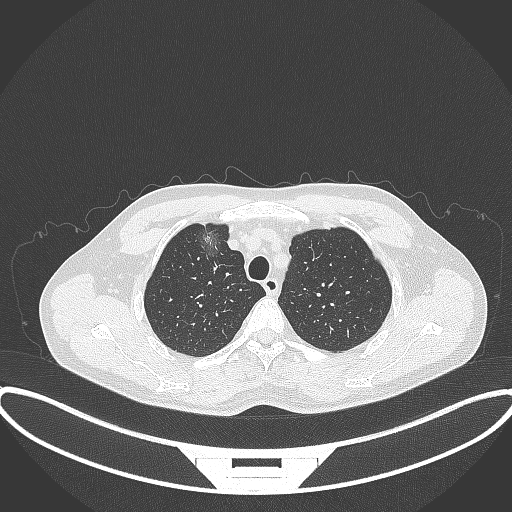
Chest CT, one axial slice. Position 297 of 395 along the scan axis. Reconstruction kernel B70f. 120 kVp. Lung window (W 1500 / L -600 HU). 1 mm slice thickness. 512 × 512 image matrix, field of view 424 × 424 mm. Patient: male, 60 years. Case-level facts recorded for this patient, not image findings: clinical TNM (as recorded): T1c N0 M0.
Outlined on this slice (bounding box drawn by a radiologist):
- lung tumour (recorded histology: adenocarcinoma): bounding box <195,218,227,268> (left, top, right, bottom; pixels)